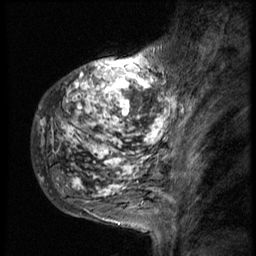
Breast MRI (dynamic contrast-enhanced), one sagittal slice. Position 14 of 58 along the scan axis. 3 images stored at this slice position (order not interpretable as contrast timing). 1.5 T. TE 4.2 ms, TR 9 ms. 2.5 mm slice thickness. 256 × 256 image matrix, field of view 180 × 180 mm. Female patient, age 50 years. From the clinical record (not read from this slice): setting: breast cancer imaged before/during neoadjuvant chemotherapy; receptor status: triple-negative.
Annotated regions visible in this slice (semi-automatic segmentation, software-assisted and operator-edited):
- analysis volume of interest (the breast-tissue region the enhancement analysis was run in; not a lesion): bounding box <33,48,186,214> (left, top, right, bottom; pixels)
- tumour enhancement mask (voxels above the 140 % enhancement threshold inside the analysis volume of interest): <37,59,186,214>